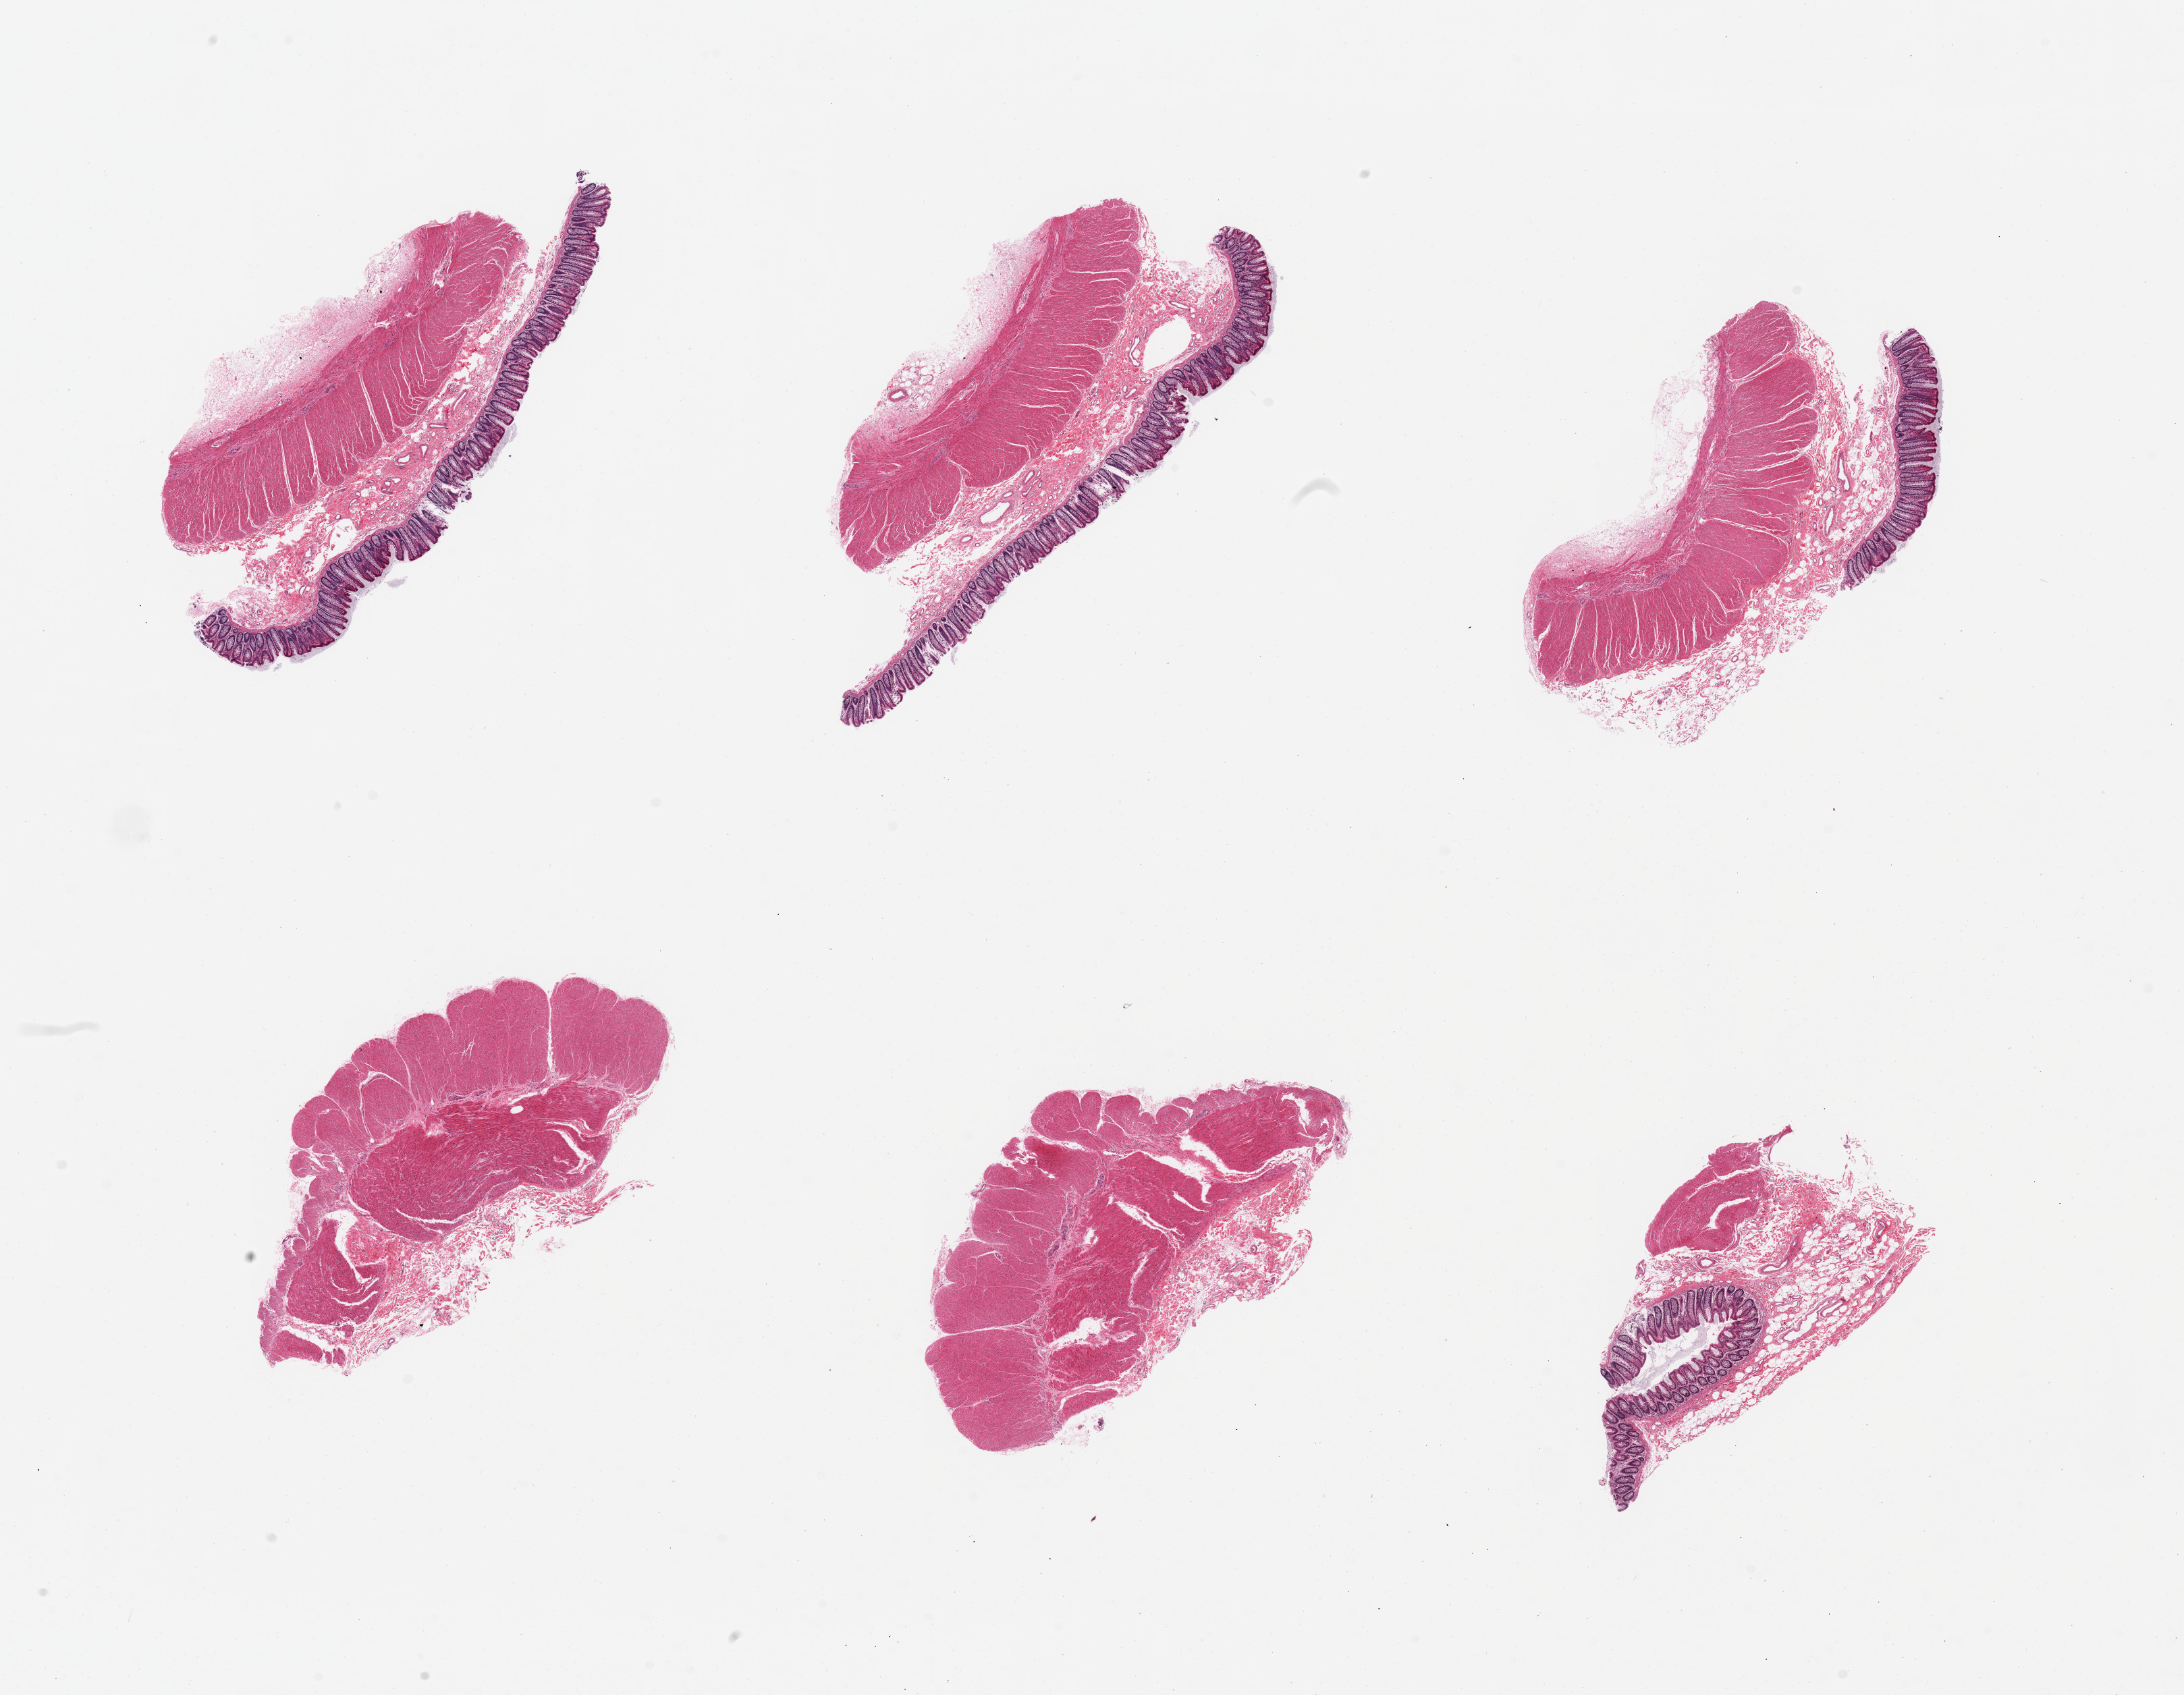
H&E whole-slide image — whole scanned area (about 25.6 x 19.9 mm) shown as a low-resolution overview, PAXgene-fixed, paraffin-embedded tissue, section of transverse colon (target tissue), donor tissue sample. Donor: male.
Review note (as recorded): 6 pieces, 4 full thickness, 2 without mucosa.